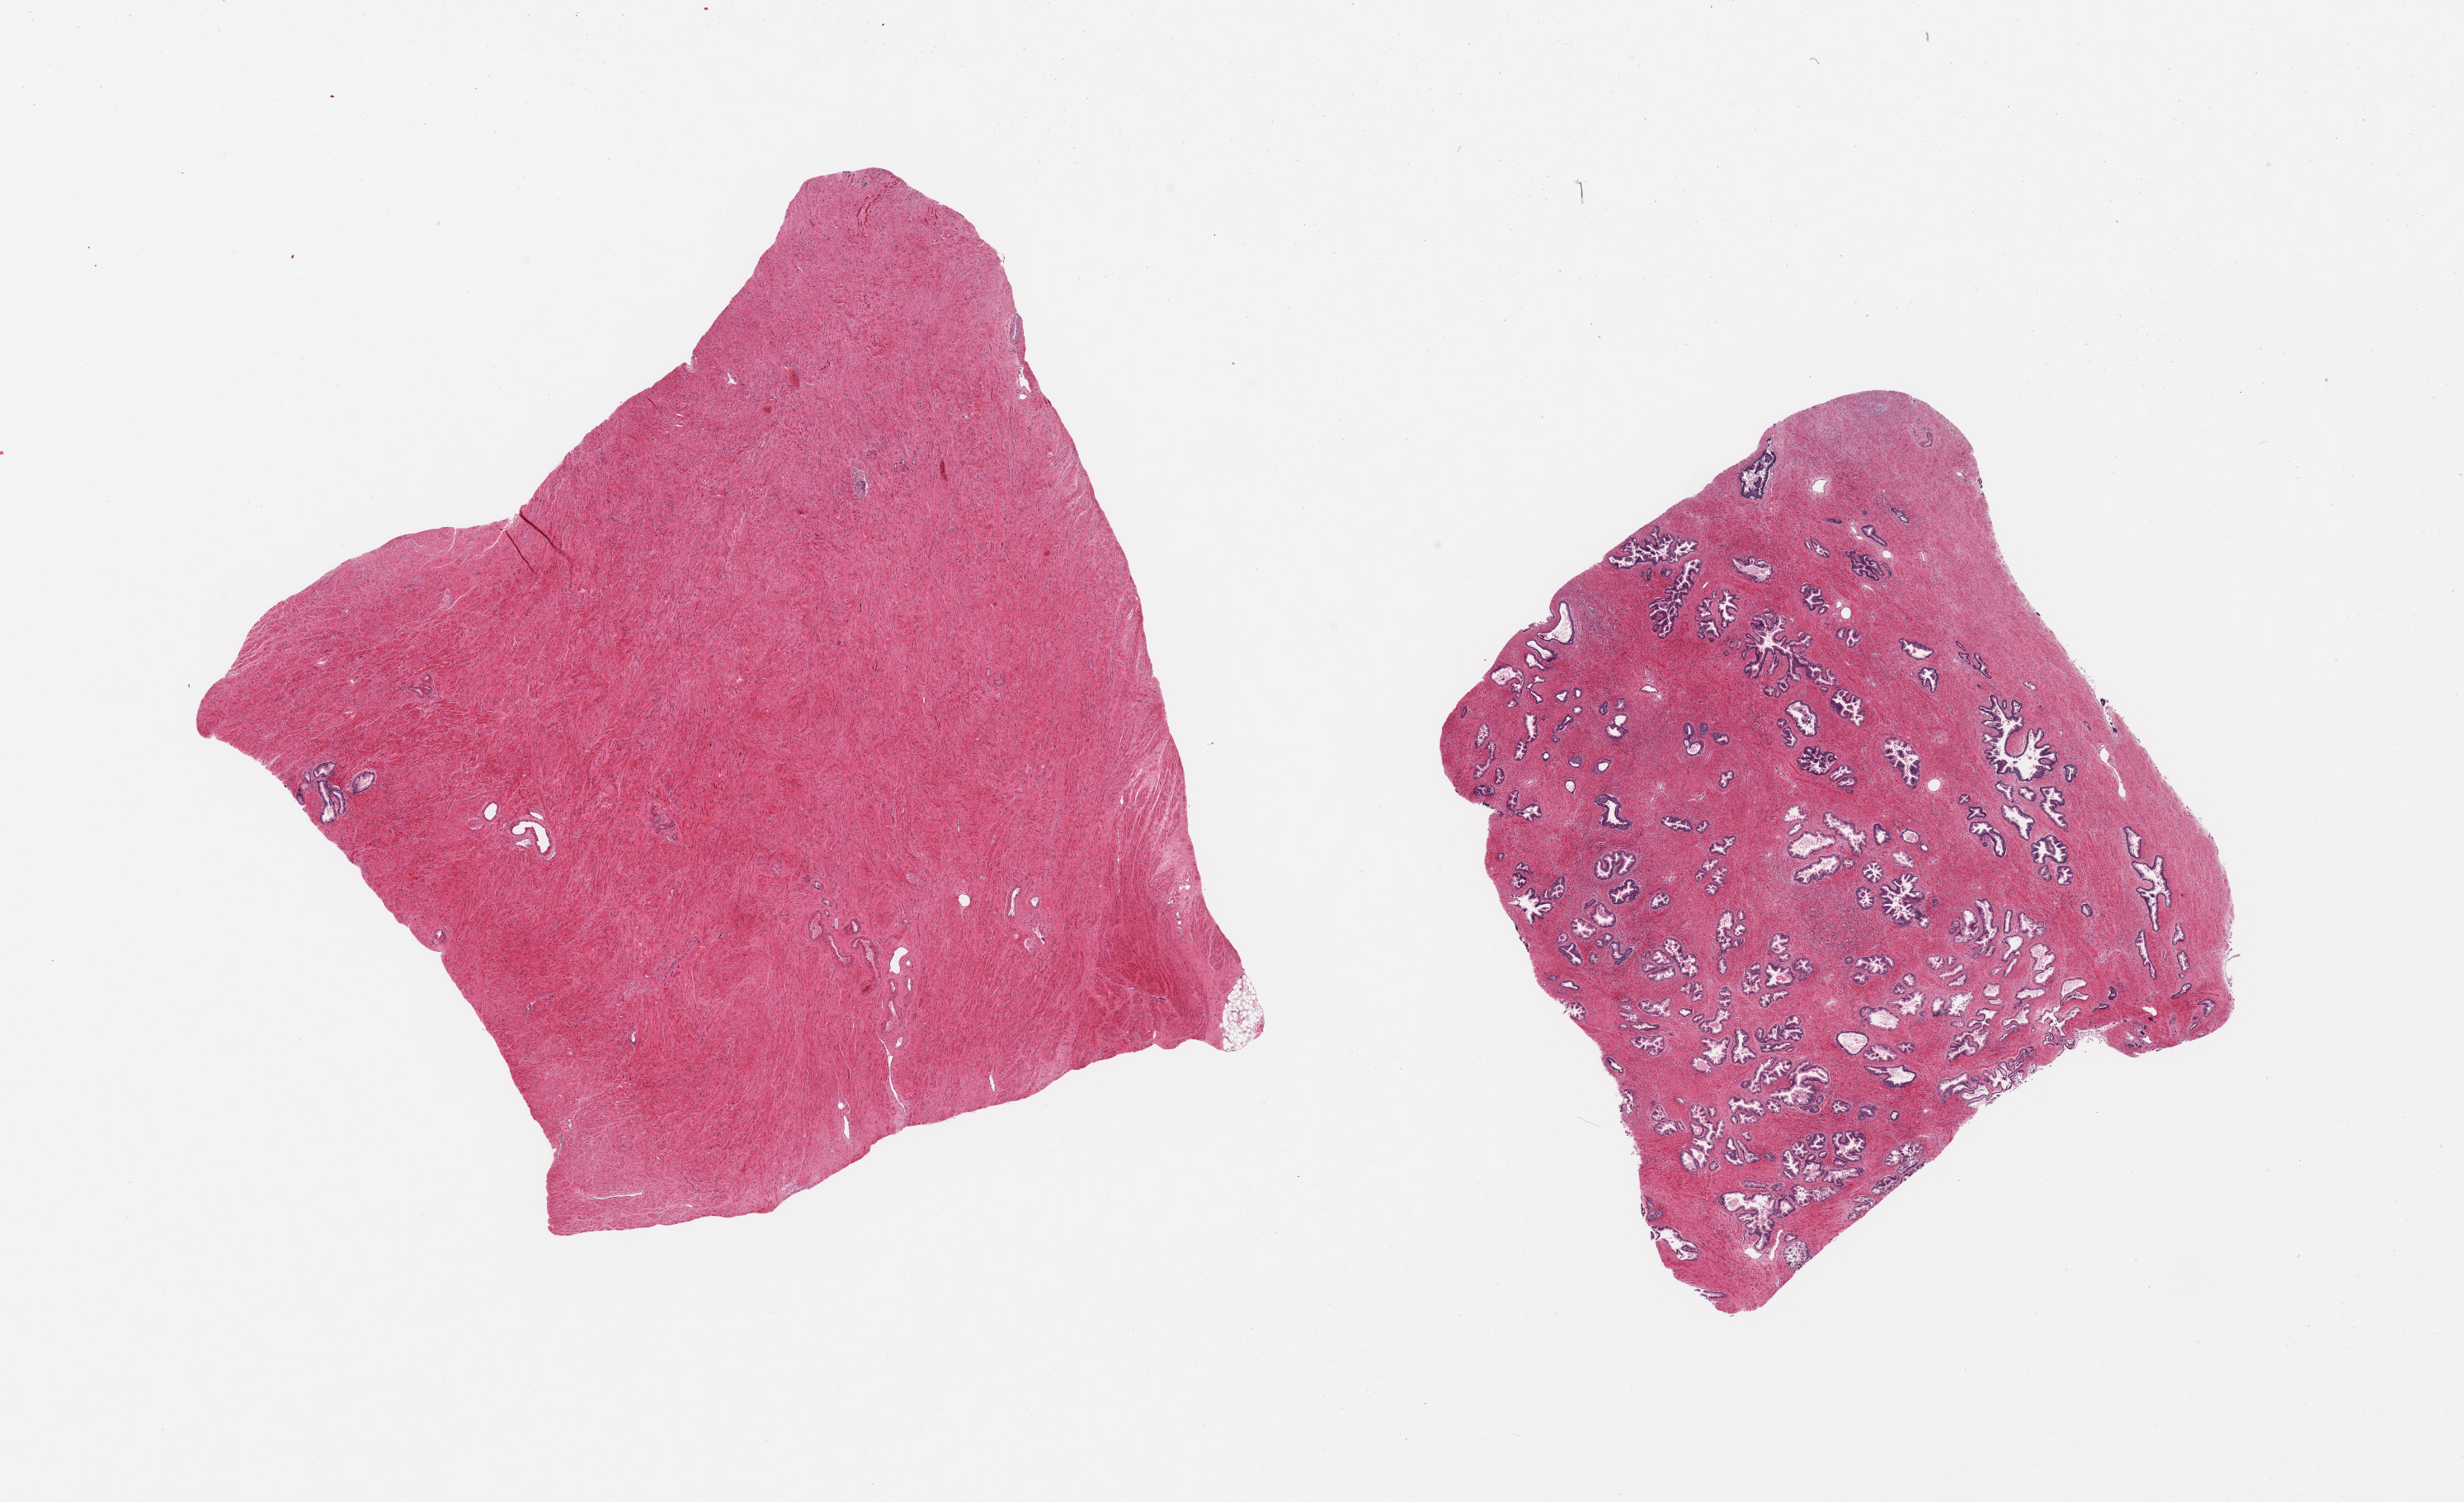
Whole-slide image, haematoxylin and eosin stain, brightfield — low-resolution overview of the scanned area, about 23.6 x 14.4 mm (from a 20x scan), PAXgene-fixed, paraffin-embedded tissue, target tissue: prostate, donor tissue sample. Donor sex: male.
Review note (as recorded): 2 pieces; one piece composed of fibromuscular stroma and a few glandular structures; other contains fibromucular stroma and glandular component.